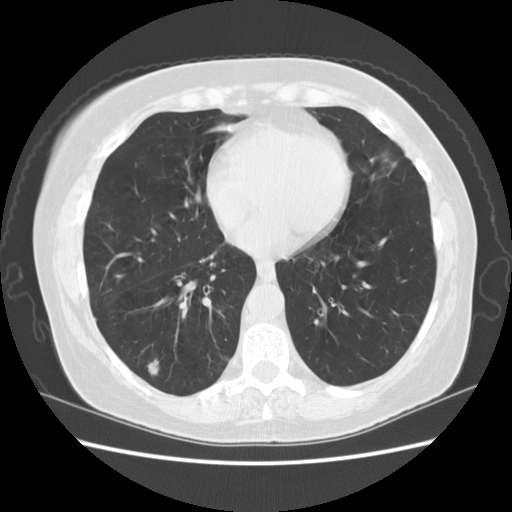
Low-dose screening chest CT, one axial slice; position 53 of 156 along the scan axis; 120 kVp; lung window (W 1500 / L -600 HU); 2.5 mm slice thickness; 512 × 512 image matrix, field of view 360 × 360 mm.
Outlined on this slice (outlined manually by an expert reader):
- lesion 1 (tumor, lower lobe of right lung): bounding box [x1, y1, x2, y2] px = [149, 360, 158, 374]